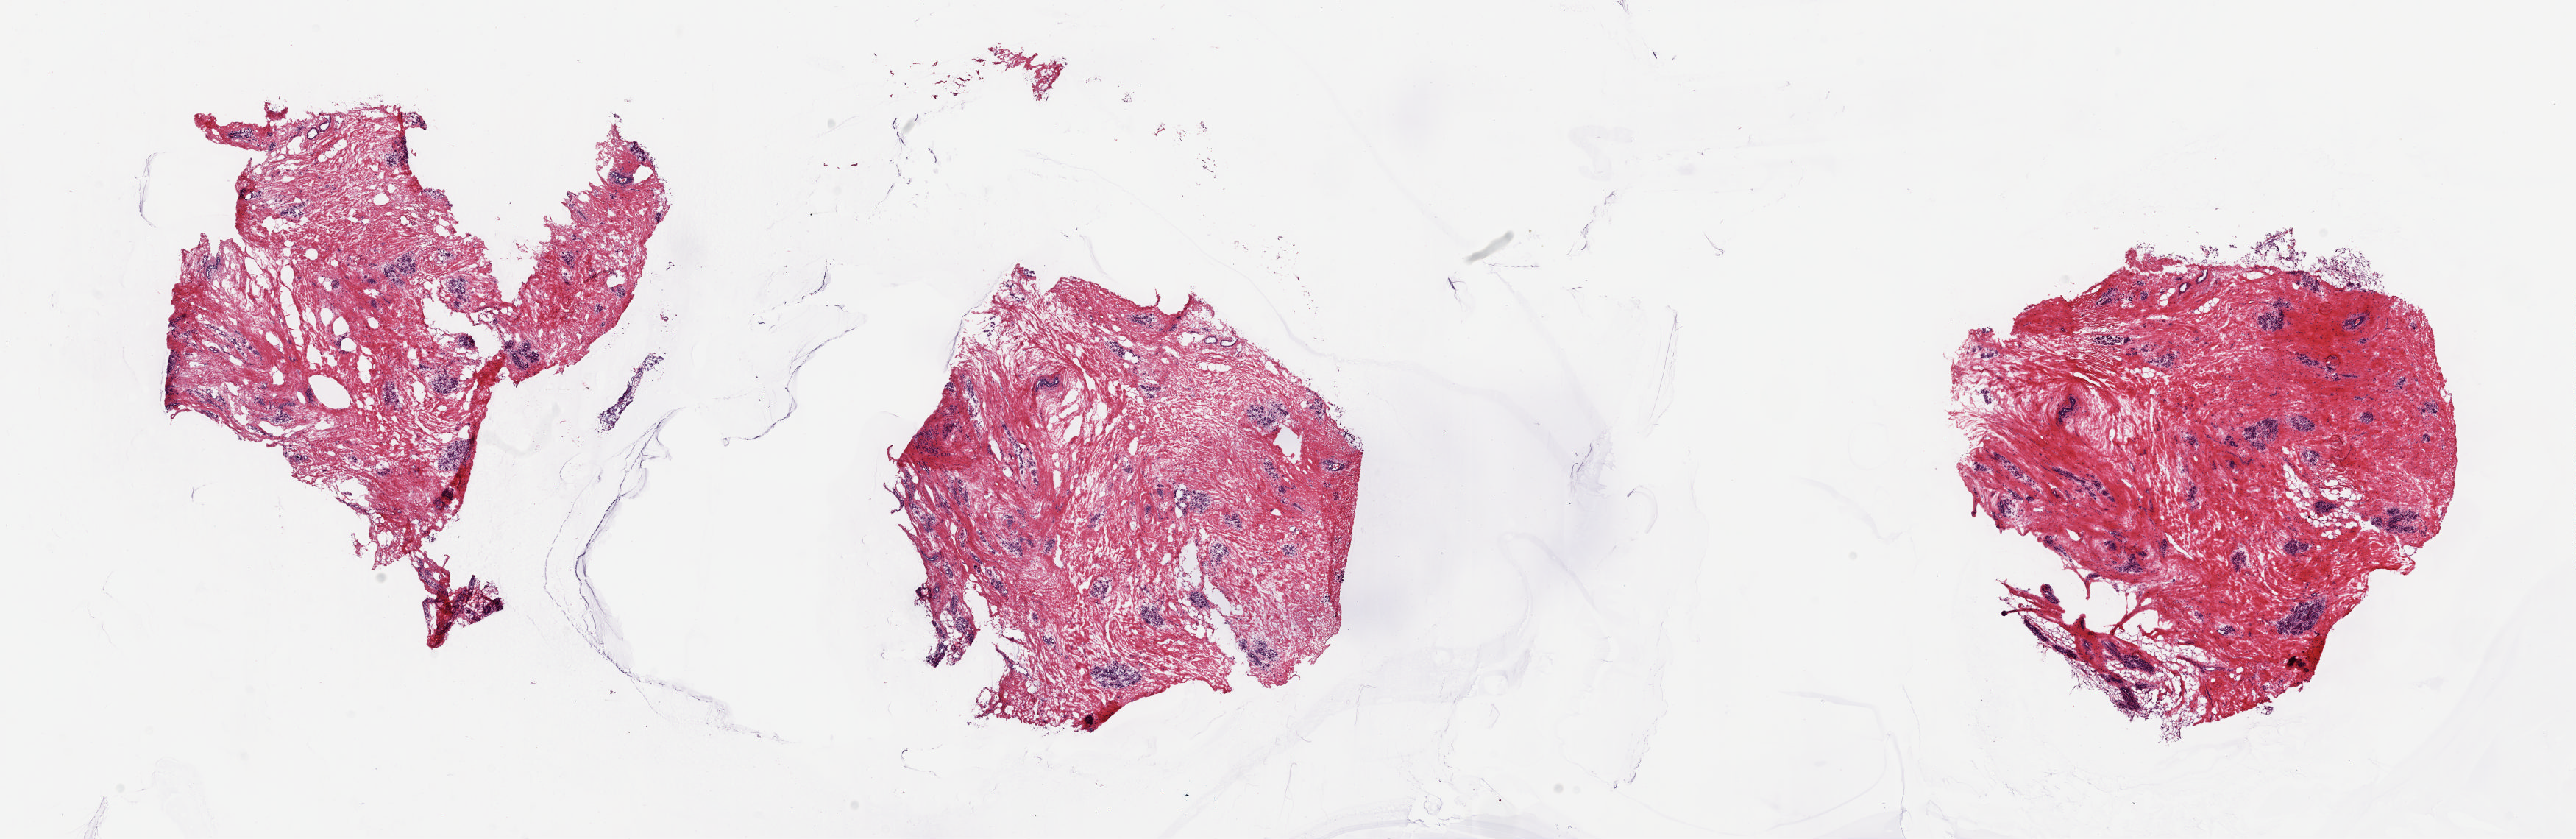
Digitized Hematoxylin and eosin (H&E) stained tissue section (whole slide), low-resolution overview of the scanned area, about 27.8 x 9.0 mm, frozen section from the bottom of the tissue portion, solid tissue normal (non-tumour tissue) sample from the breast. Patient: female, age at initial diagnosis 40 years.
This section: solid tissue normal sample (biorepository sample class). Patient diagnosis: Lobular carcinoma, NOS.